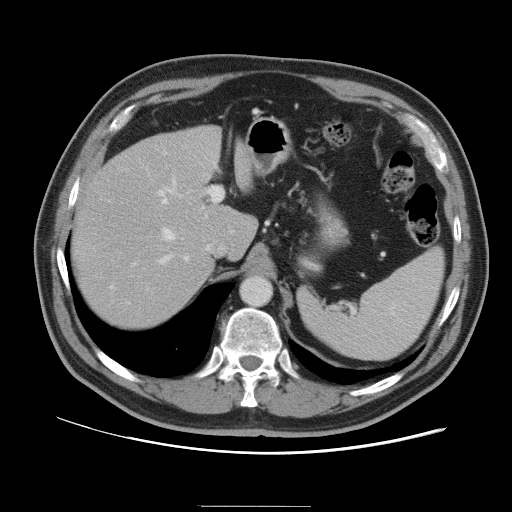
Contrast-enhanced abdominal CT, one axial slice. Slice 71 of 105 in the series (ordered by position). 120 kVp. Intravenous contrast given. Soft-tissue window (W 400 / L 40 HU). 512 × 512 image matrix. Male patient, age 64 years. From the clinical record (not read from this slice): diagnosis: colorectal cancer liver metastases, imaged before liver resection; multiple liver metastases: yes; largest metastasis: 3 cm.
Annotated regions visible in this slice (expert manual segmentation):
- hepatic veins: box from (x=161, y=180) to (x=182, y=263) px
- liver: (x=73, y=127)–(x=255, y=328)
- planned liver remnant (the part of the liver to remain after resection): (x=73, y=141)–(x=255, y=328)
- portal vein (with intrahepatic branches): (x=110, y=174)–(x=223, y=289)